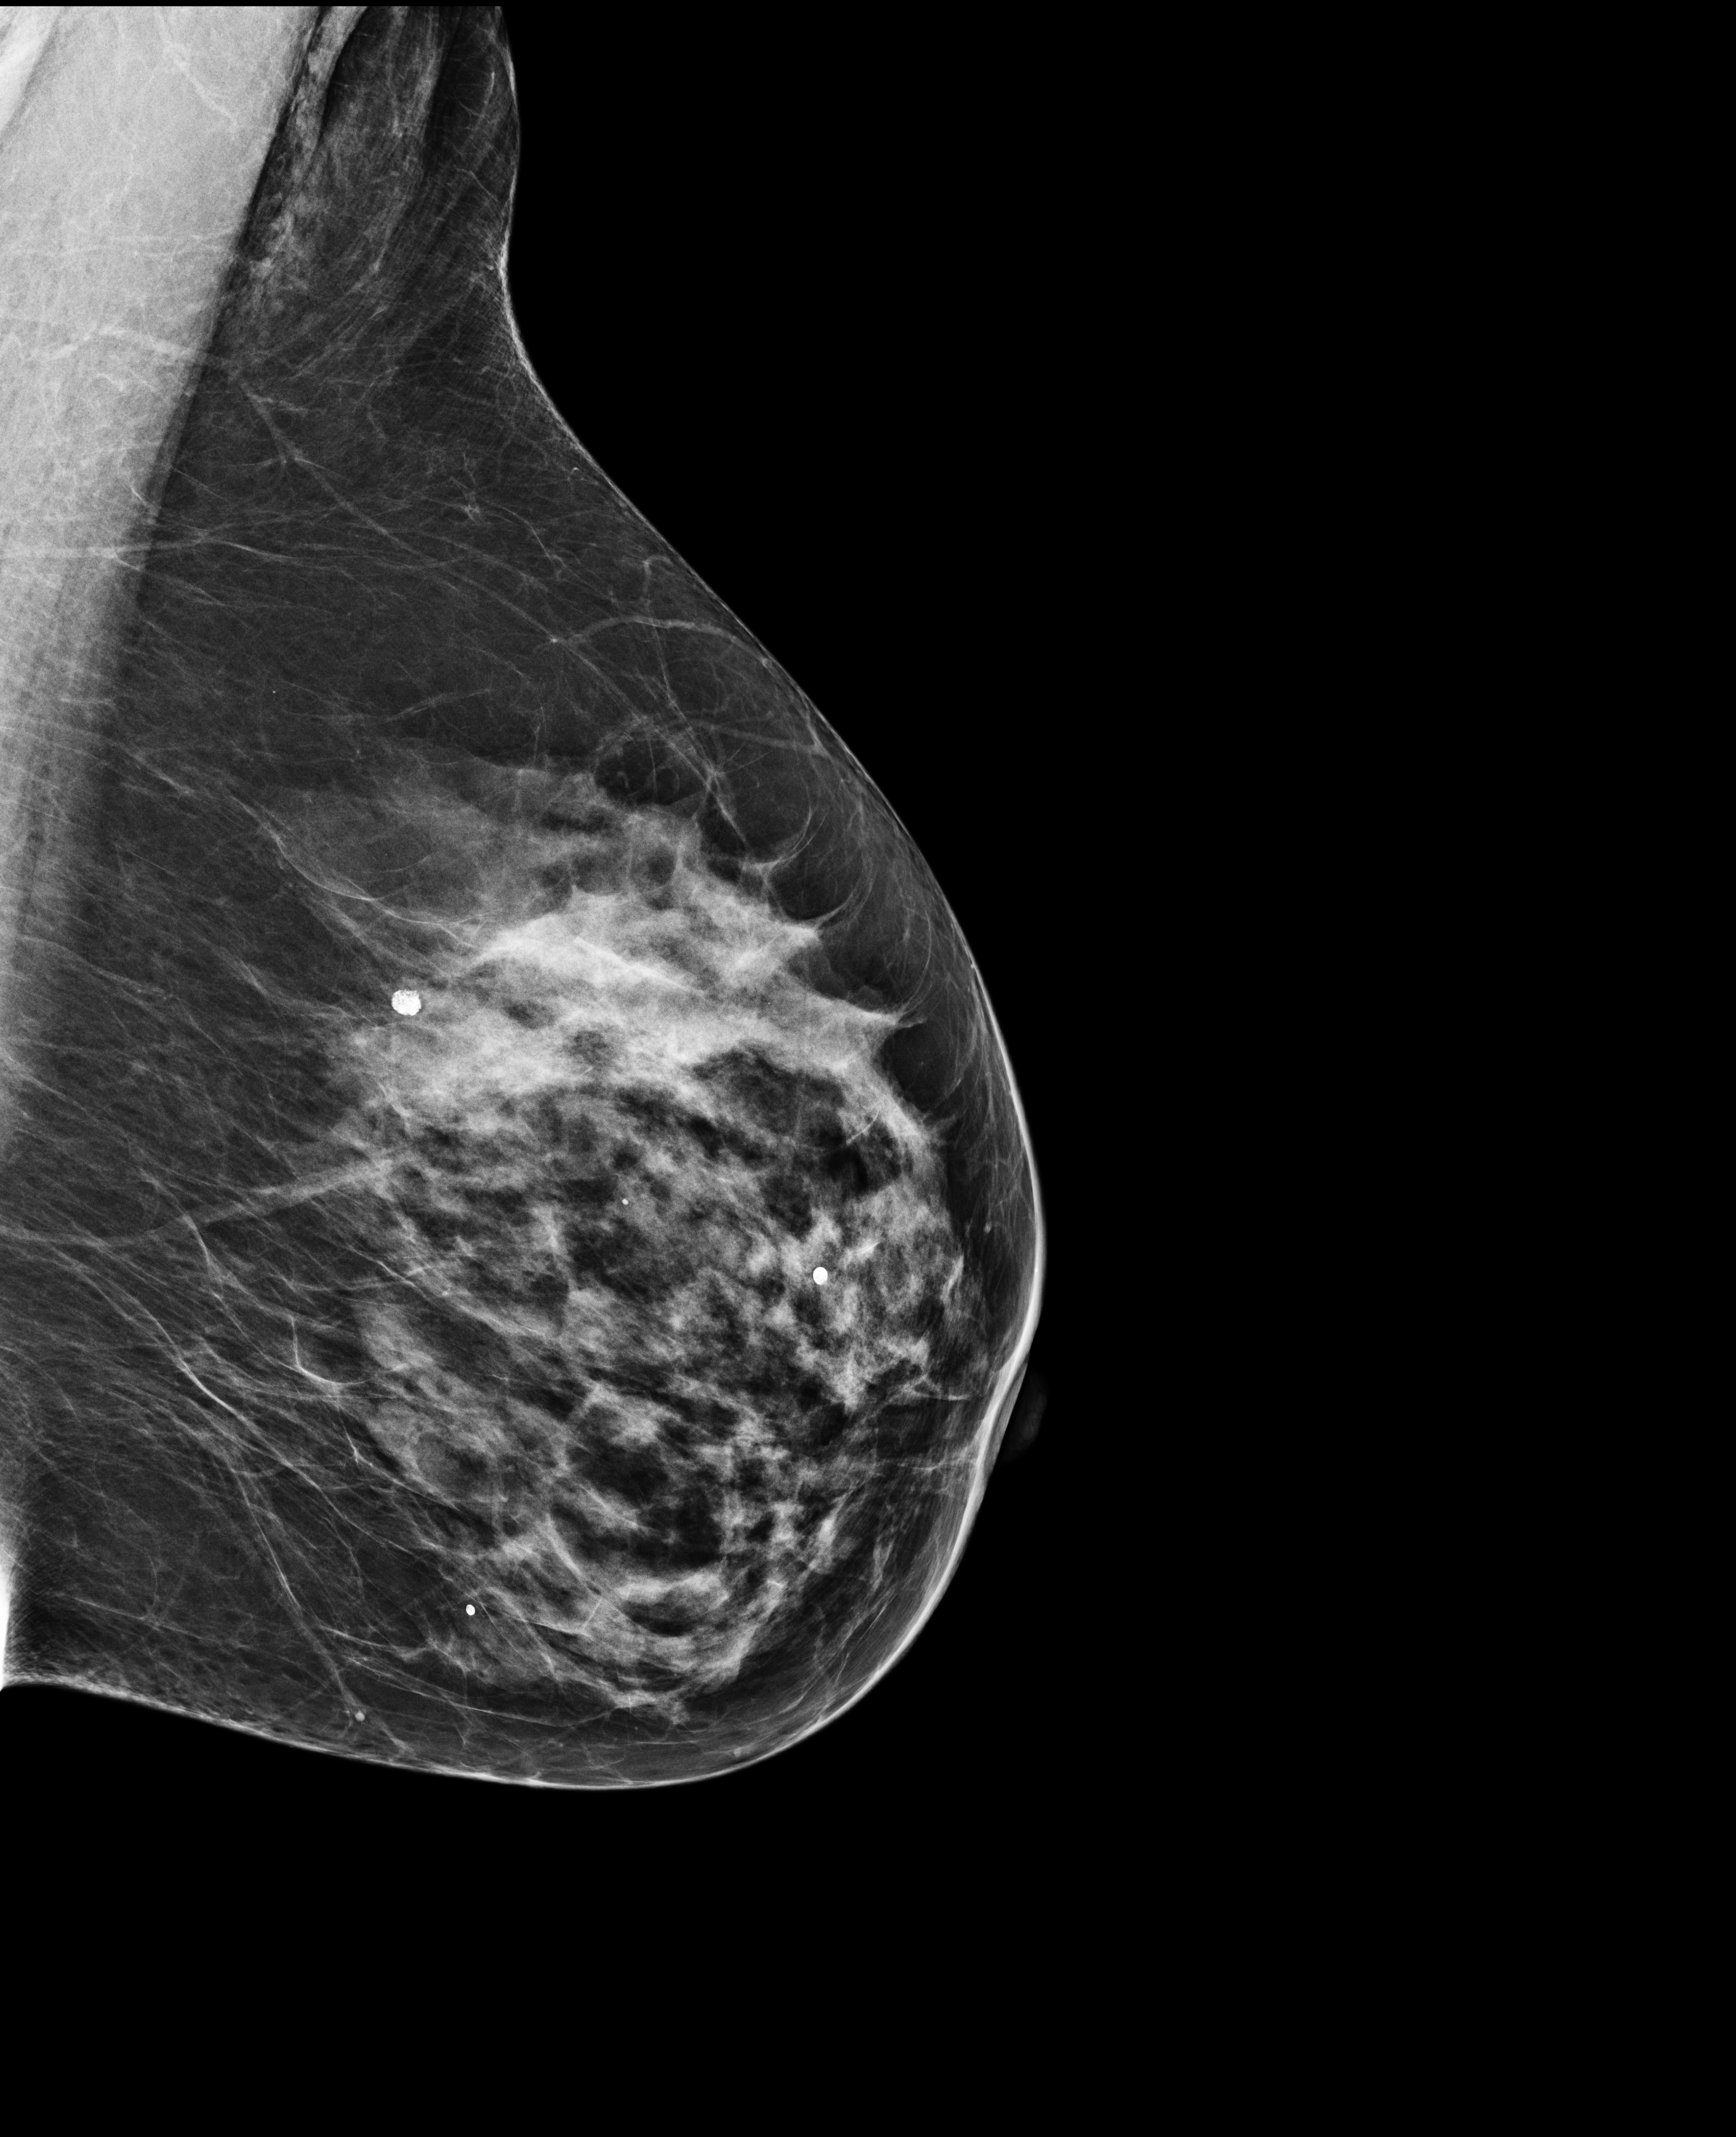
Screening examination, system: Selenia Dimensions. Female patient, age 63 years.
Image type: full-field digital mammogram. Breast: left. Projection: MLO view.